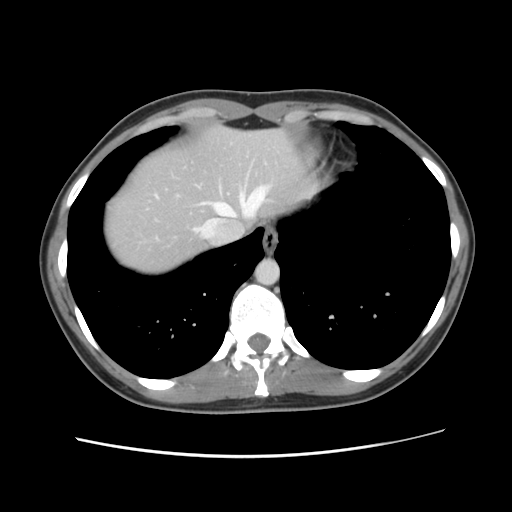
Contrast-enhanced abdominal CT, one axial slice. Slice 108 of 134 in the series (ordered by position). 120 kVp. Intravenous contrast given. Soft-tissue window (W 400 / L 40 HU). 2.5 mm slice thickness. 512 × 512 image matrix. Female patient, age 33 years. From the clinical record (not read from this slice): diagnosis: colorectal cancer liver metastases, imaged before liver resection; multiple liver metastases: yes; largest metastasis: 4.5 cm; chemotherapy before resection: no.
Structures marked on this image (manually delineated by an expert):
- hepatic veins: box from (x=194, y=187) to (x=268, y=238) px
- liver: (x=104, y=126)–(x=316, y=274)
- planned liver remnant (the part of the liver to remain after resection): (x=104, y=126)–(x=316, y=274)